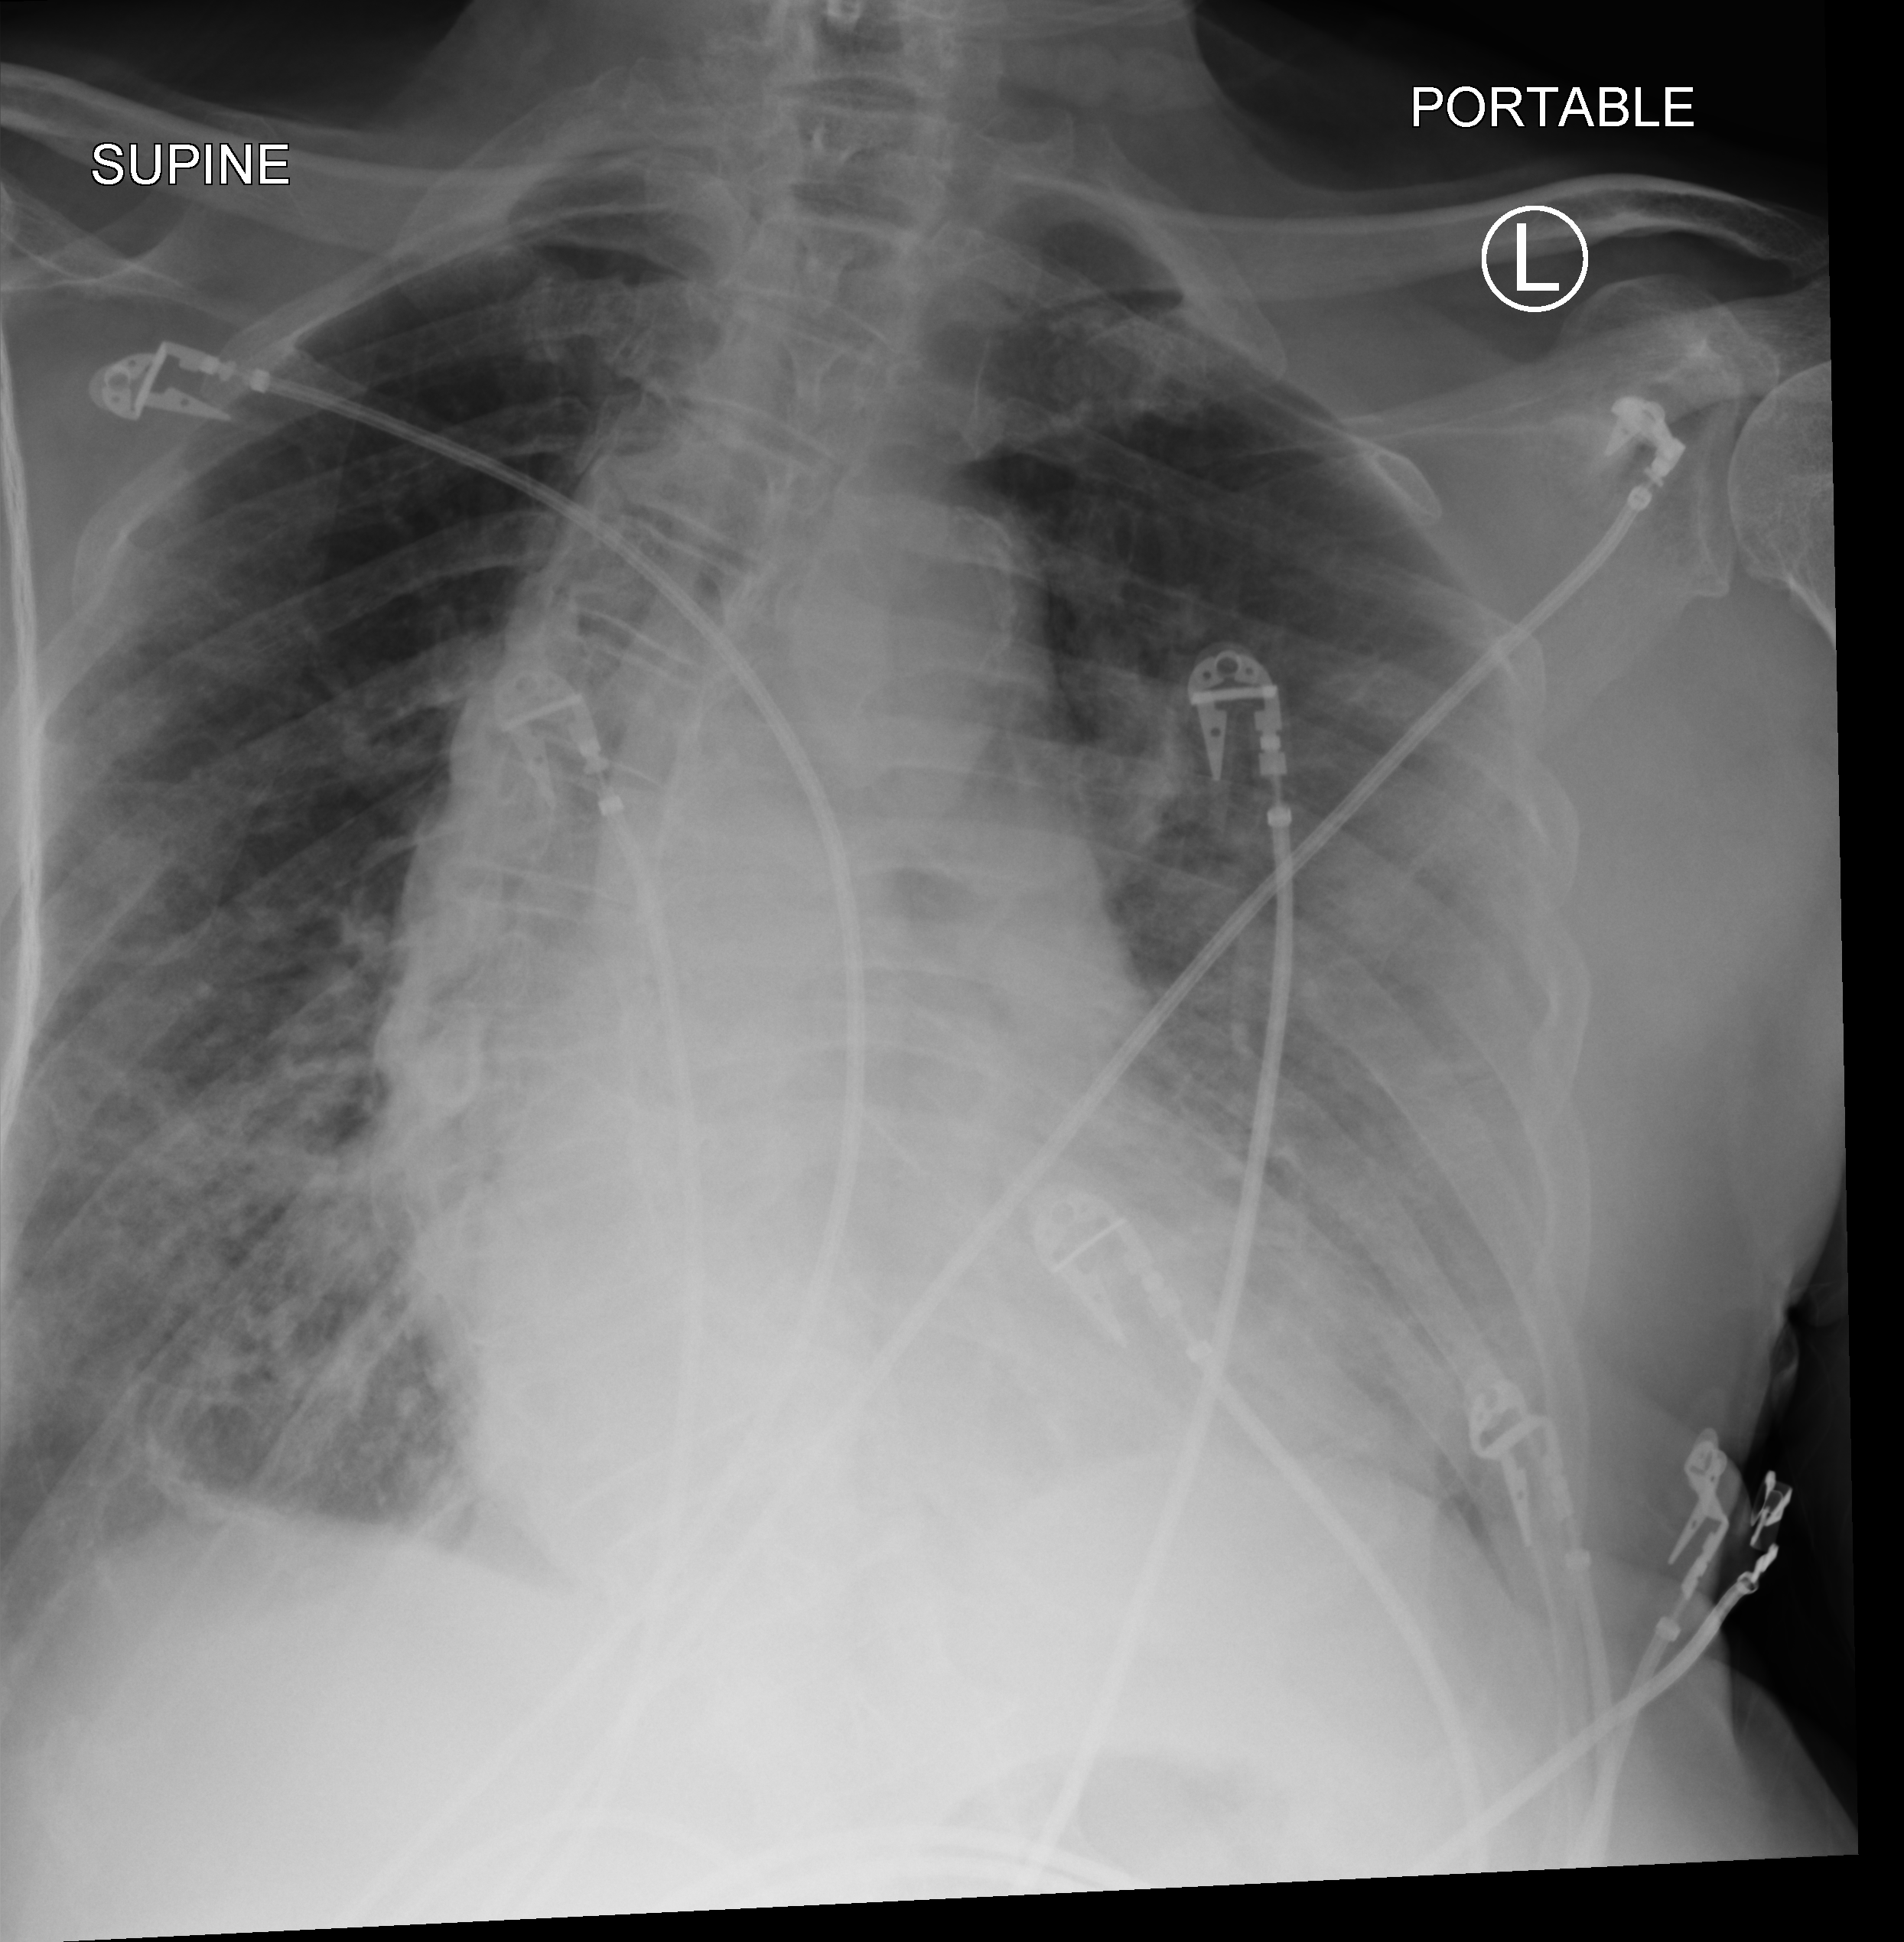
Portable chest radiograph; anteroposterior (AP) projection. Patient hospitalised with COVID-19; male, aged 75–90 years.
Hospital-stay facts (about this admission, not read from this image; timing relative to this image not recorded):
- length of hospital stay: 12 days
- mechanically ventilated during this hospital stay: no